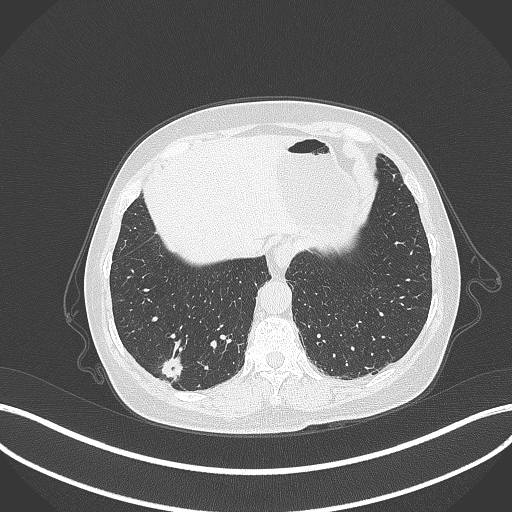
Chest CT, one axial slice. Slice 57 of 333 in the series (ordered by position). 120 kVp. Lung window (W 1500 / L -600 HU). 512 × 512 image matrix. Patient: female, 69 years. From the clinical record (not read from this slice): clinical TNM (as recorded): T1b N0 M0; histopathological grade: G2-3.
Structures marked on this image (bounding box drawn by a radiologist):
- lung tumour (recorded histology: adenocarcinoma): bounding box <158,350,184,379> (left, top, right, bottom; pixels)